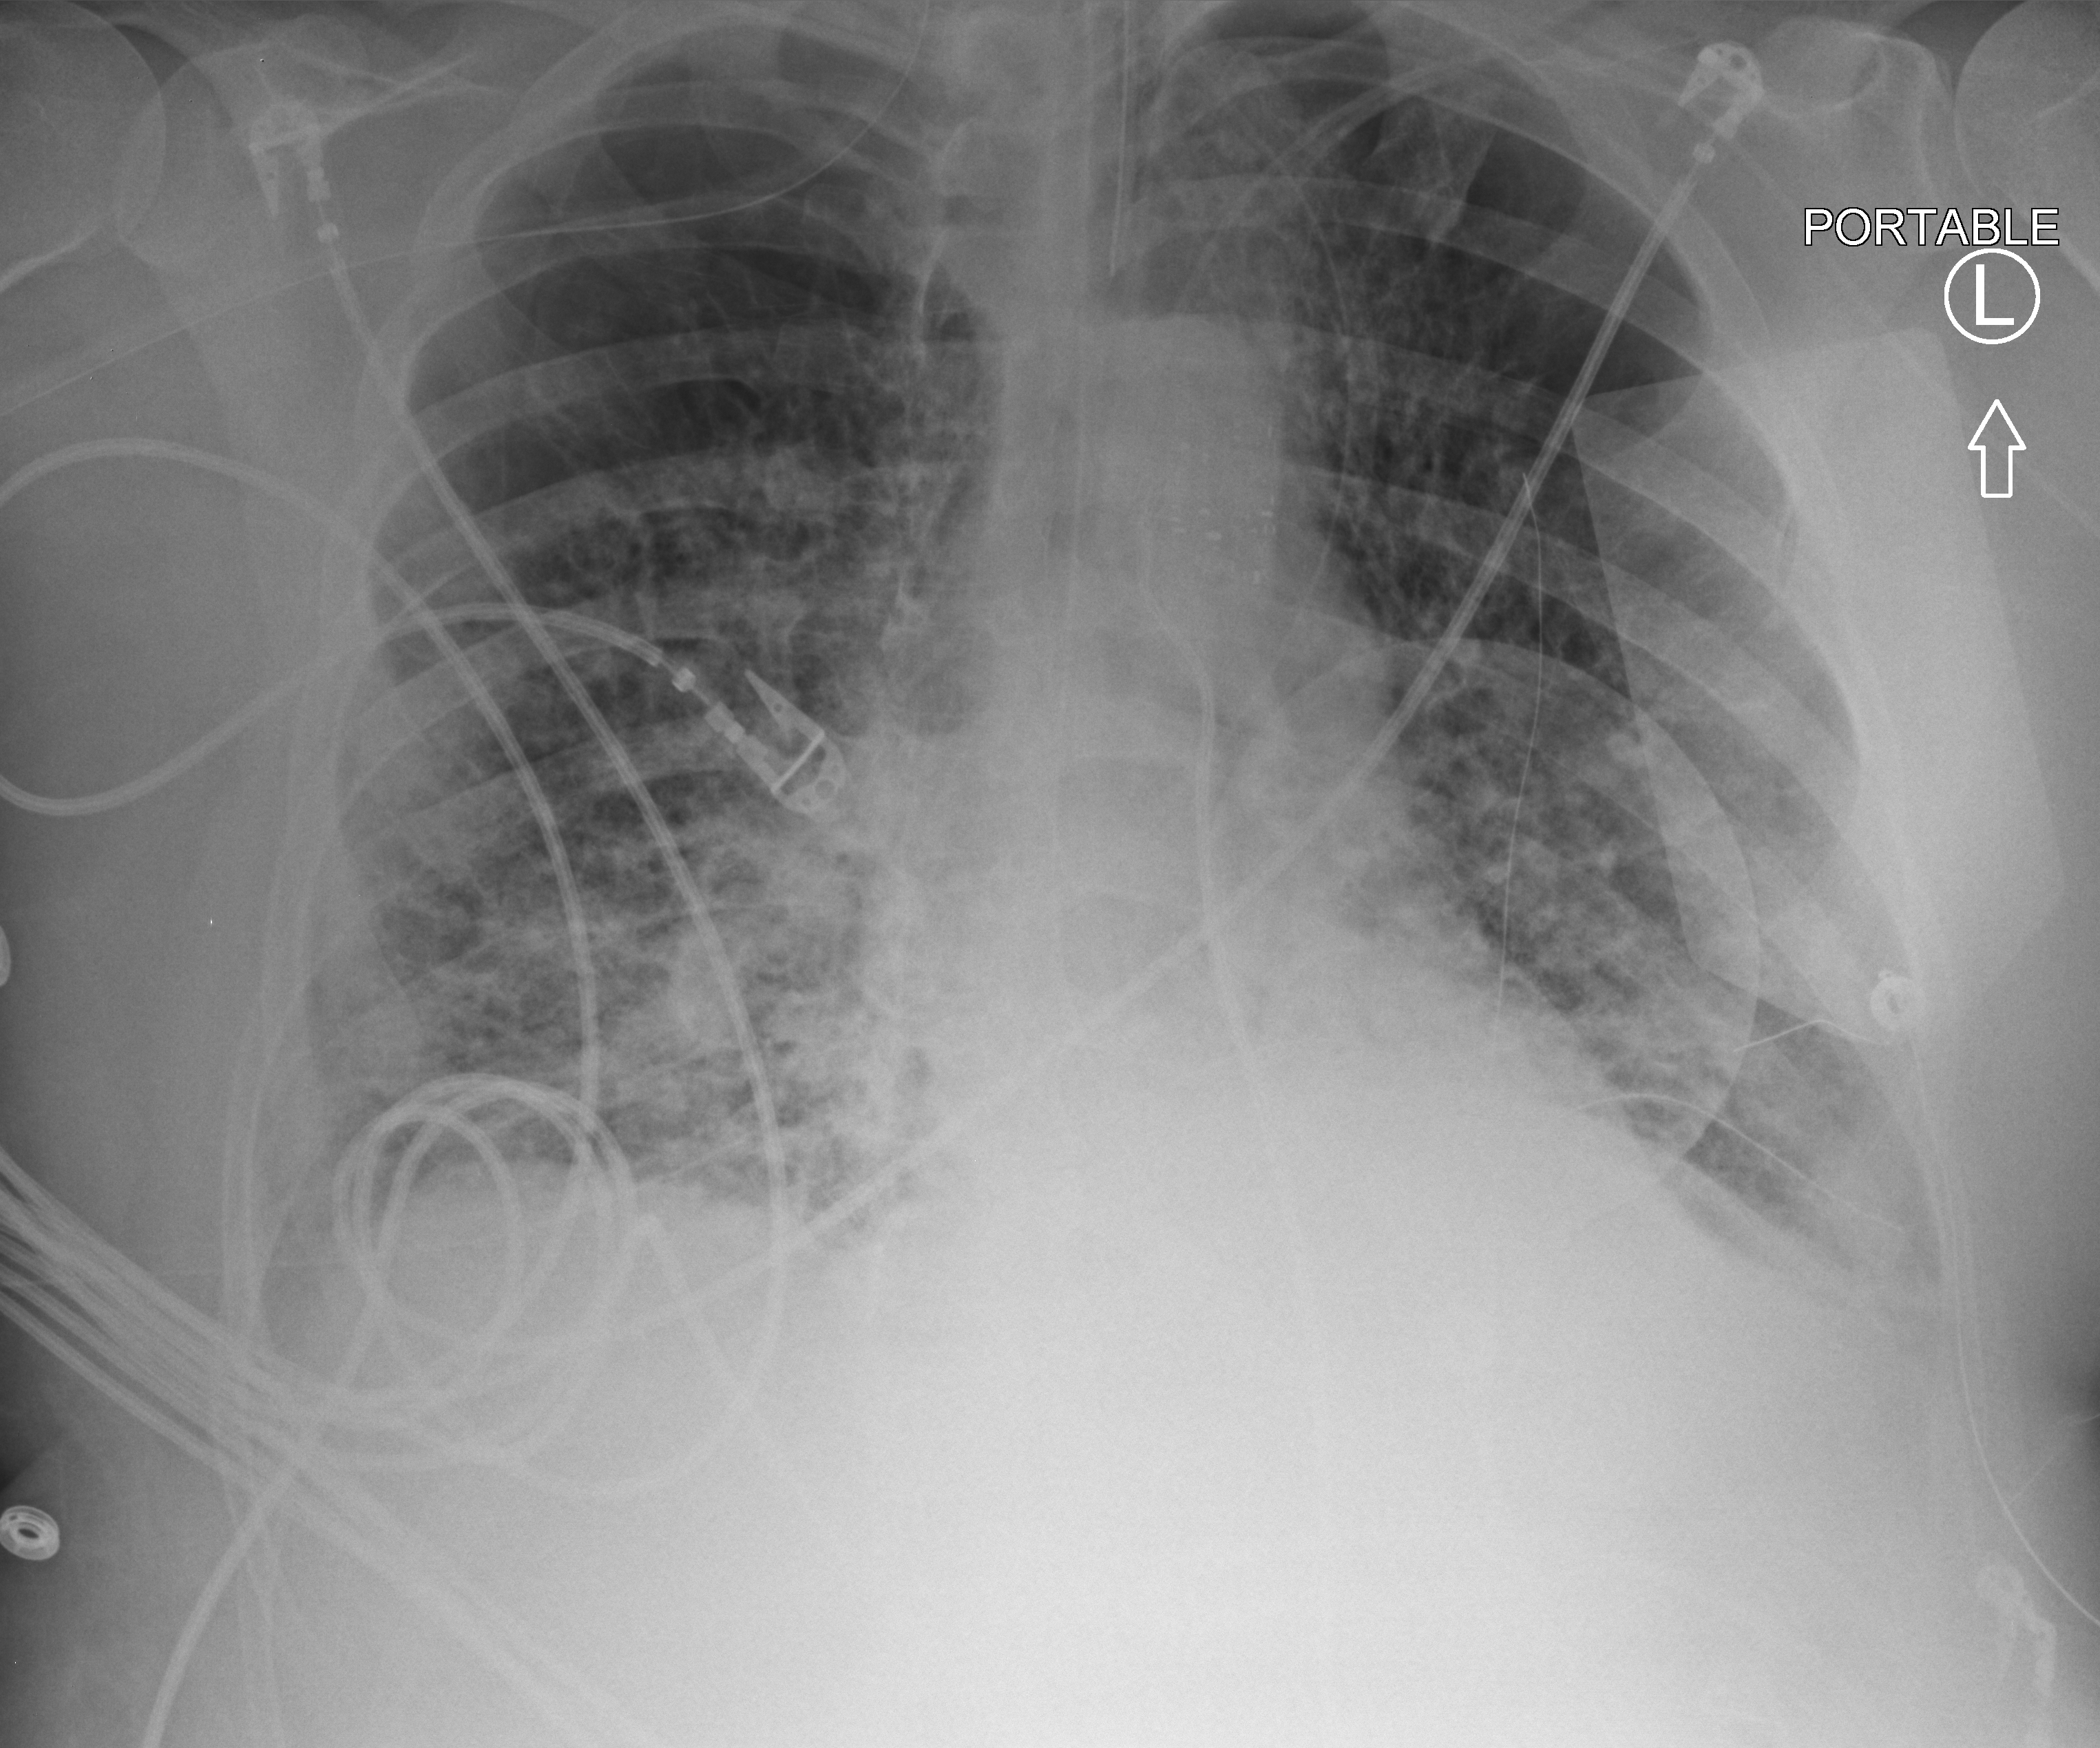
Bedside chest radiograph (computed radiography), anteroposterior (AP) projection. Patient hospitalised with COVID-19, aged 18–59 years.
Admission-level facts for this patient (not findings on this image; timing relative to this image not recorded): mechanically ventilated during this hospital stay: yes; diabetes (admission record): no; admitted to intensive care during this hospital stay: yes.